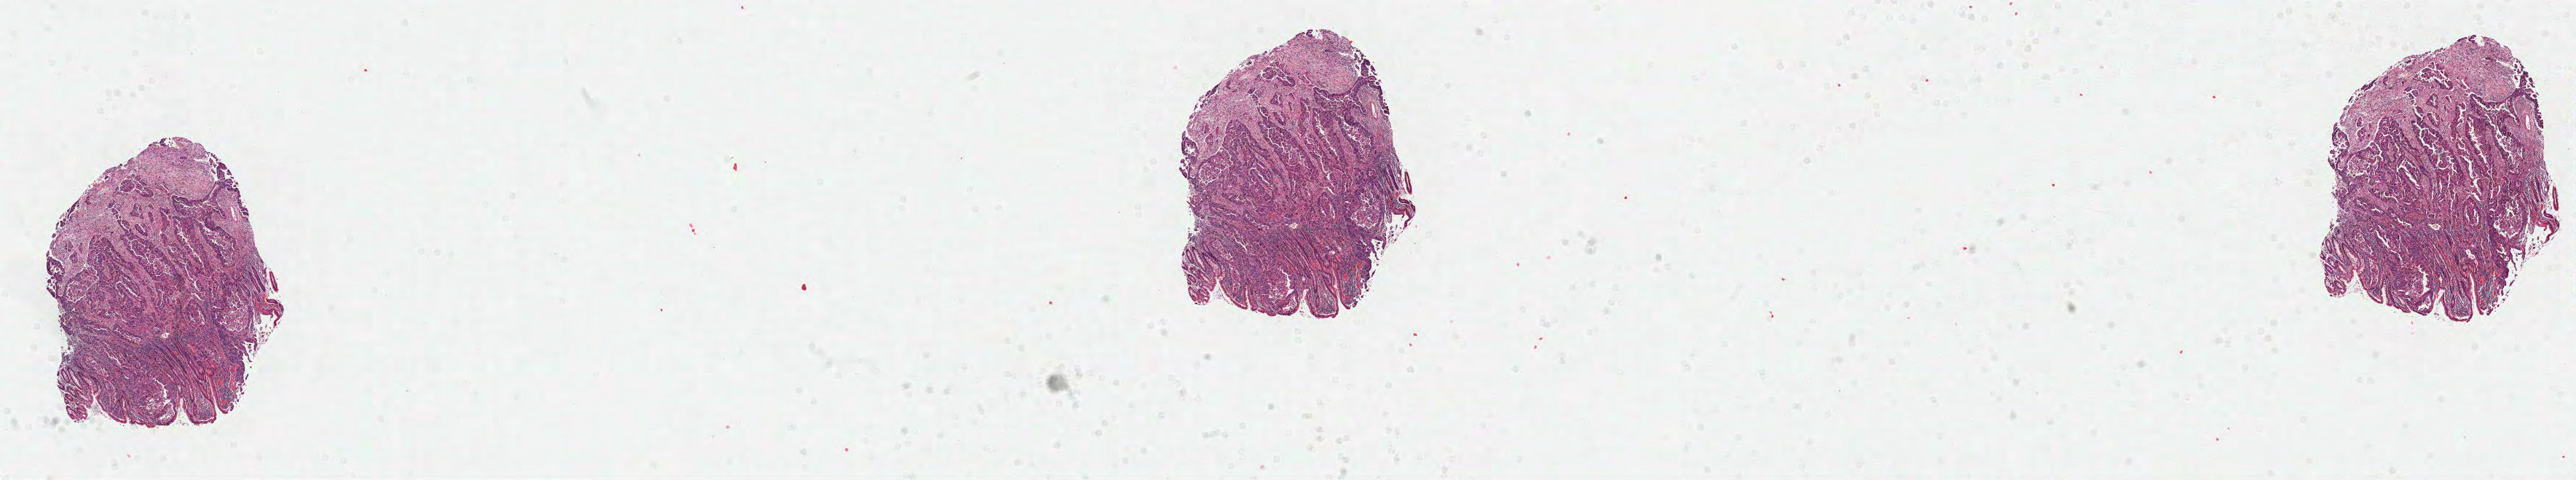
Hematoxylin and eosin (H&E) stained whole-slide image, shown as a low-resolution overview of the whole scanned area (about 28.5 x 5.3 mm, acquisition: 40x scan); formalin-fixed paraffin-embedded (FFPE) diagnostic section; colon, primary tumour sample. Patient: female, age at initial diagnosis 50 years.
Pathologic diagnosis: Adenocarcinoma, NOS (ascending colon).